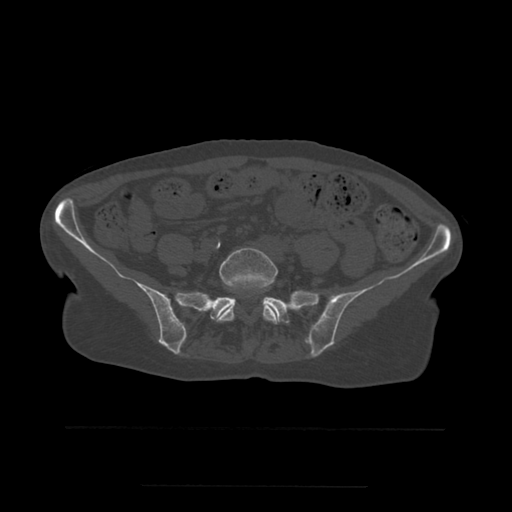
CT including the spine, one axial slice; slice 137 of 544 in the series (ordered by position); bone window (W 1800 / L 400 HU); 512 × 512 image matrix, field of view 350 × 350 mm. Patient age 58 years. From the clinical record (not read from this slice): primary cancer: lung.
Annotated regions visible in this slice (semi-automatic segmentation, software-assisted and operator-edited):
- L5 vertebra: bounding box <217,248,279,324> (left, top, right, bottom; pixels)